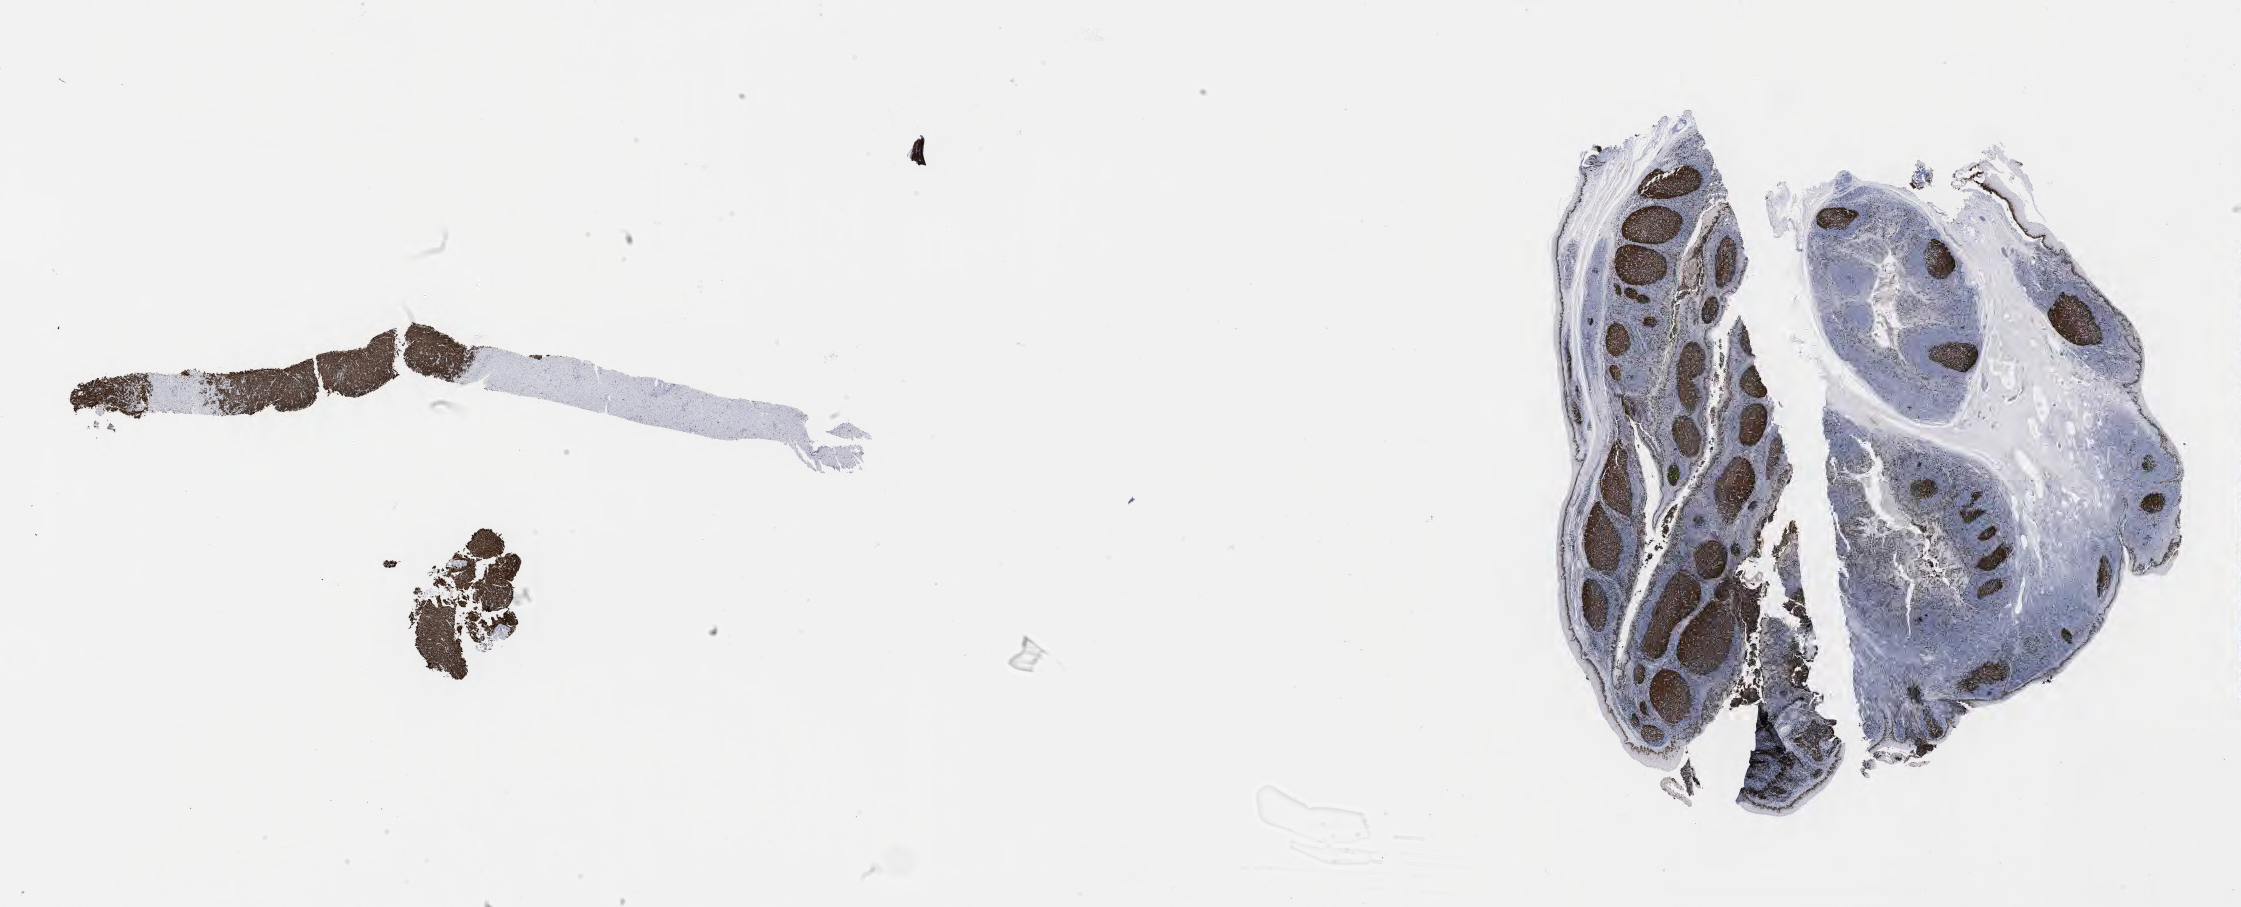
Immunohistochemistry (IHC) whole-slide image stained for Ki-67, a low-resolution overview of the entire scanned area, about 36.2 x 14.7 mm; specimen: tumor tissue. Patient male; 68 years old.
Diagnosis: Burkitt lymphoma, NOS.